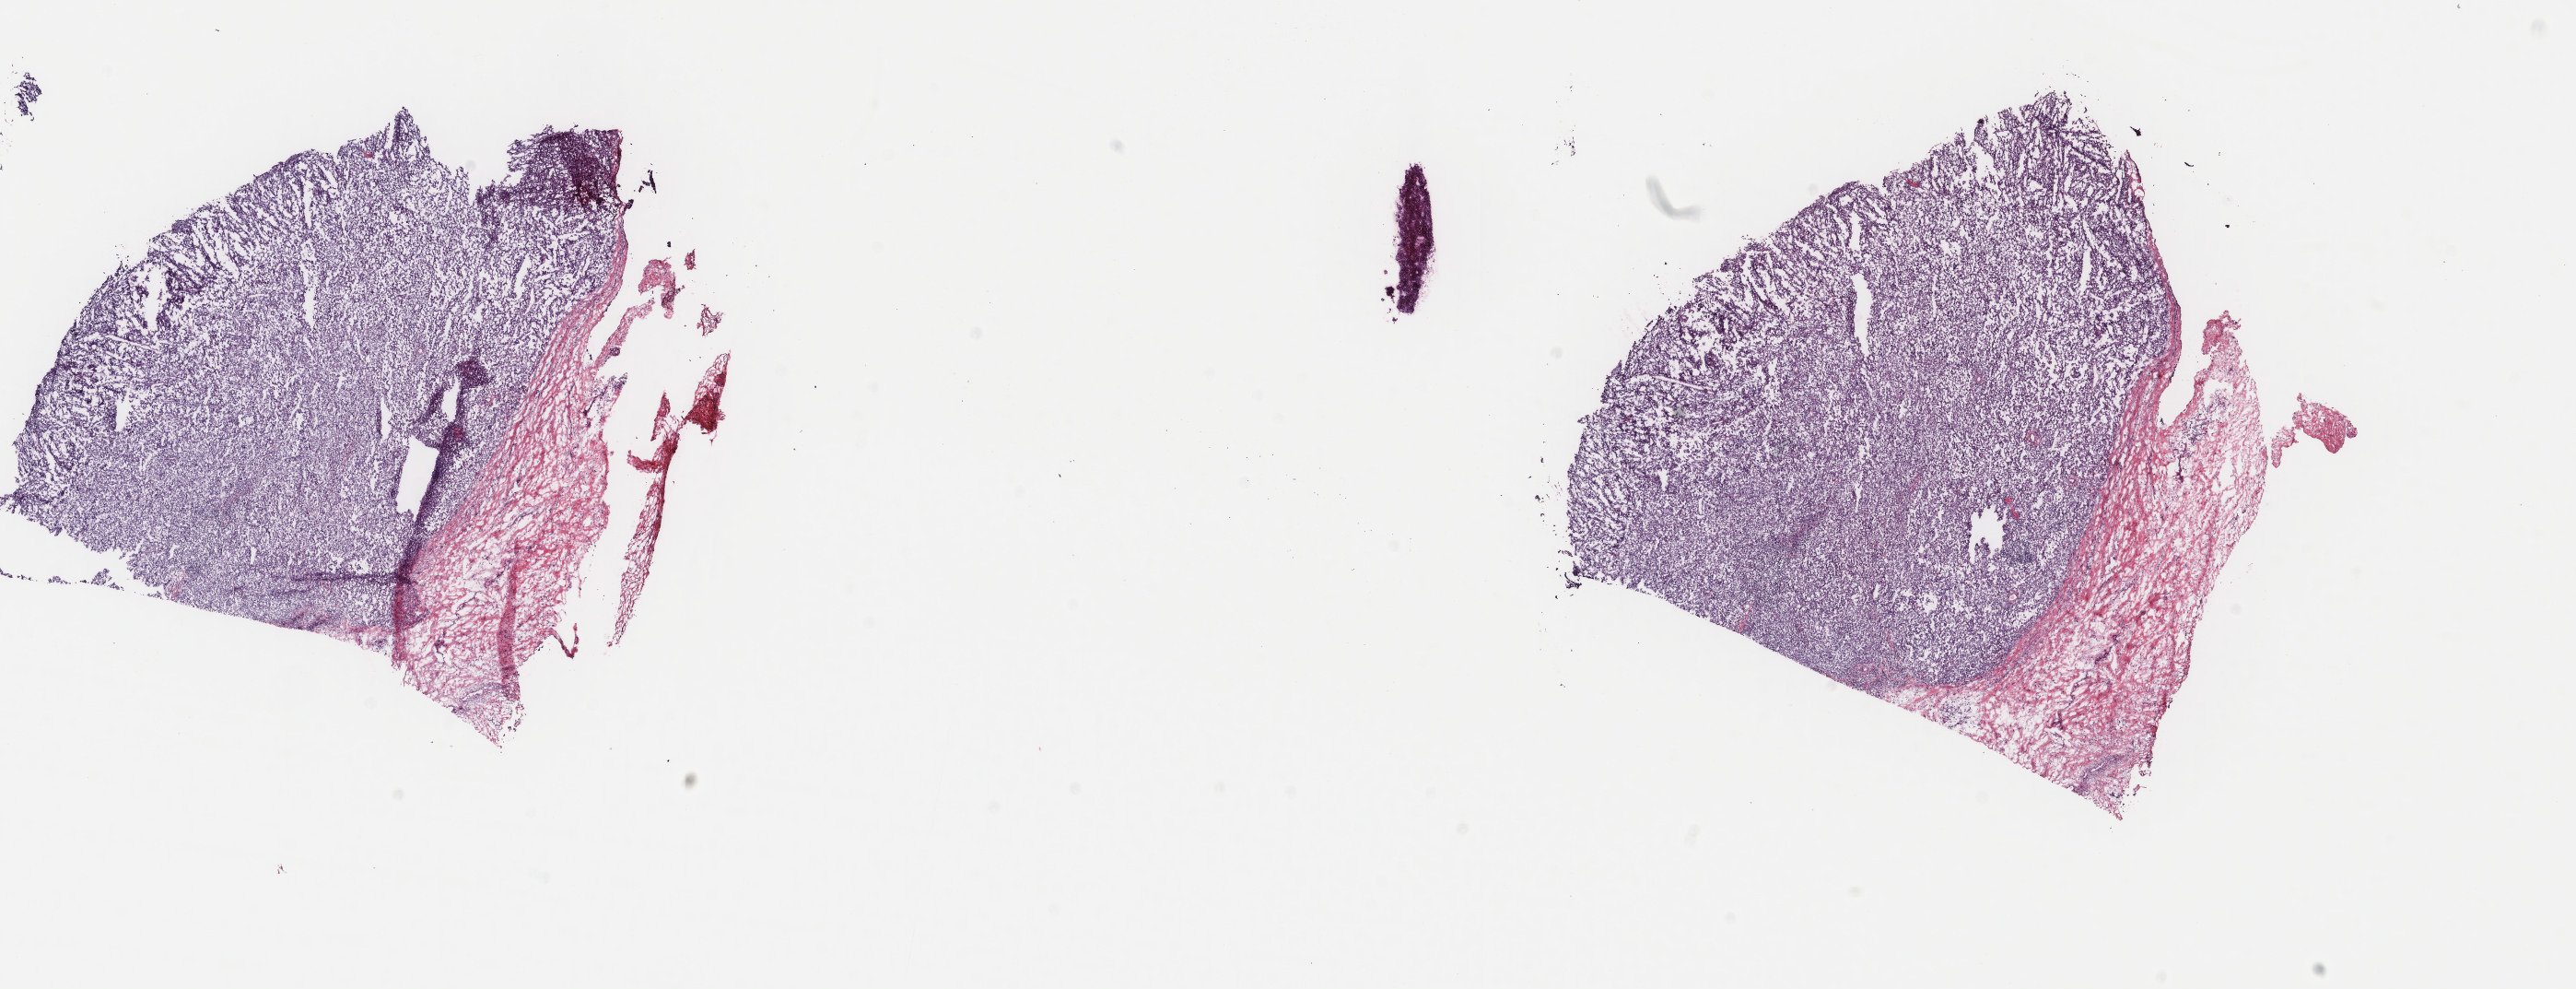
H&E-stained whole-slide image — low-resolution overview of the scanned area, about 22.2 x 8.5 mm (slide scanned at 40x); frozen section from the top of the tissue portion; metastatic tumour sample. Male patient; age at initial diagnosis 52 years. Pathologist review of this section (percent, as recorded): tumour cells 85%, tumour nuclei 95%, normal cells 0%, stromal cells 15%, necrosis 0%. Infiltration values recorded for this section: lymphocyte infiltration 0%, monocyte infiltration 0%, neutrophil infiltration 0%.
This section: metastatic tumour tissue. Patient diagnosis: Malignant melanoma, NOS.